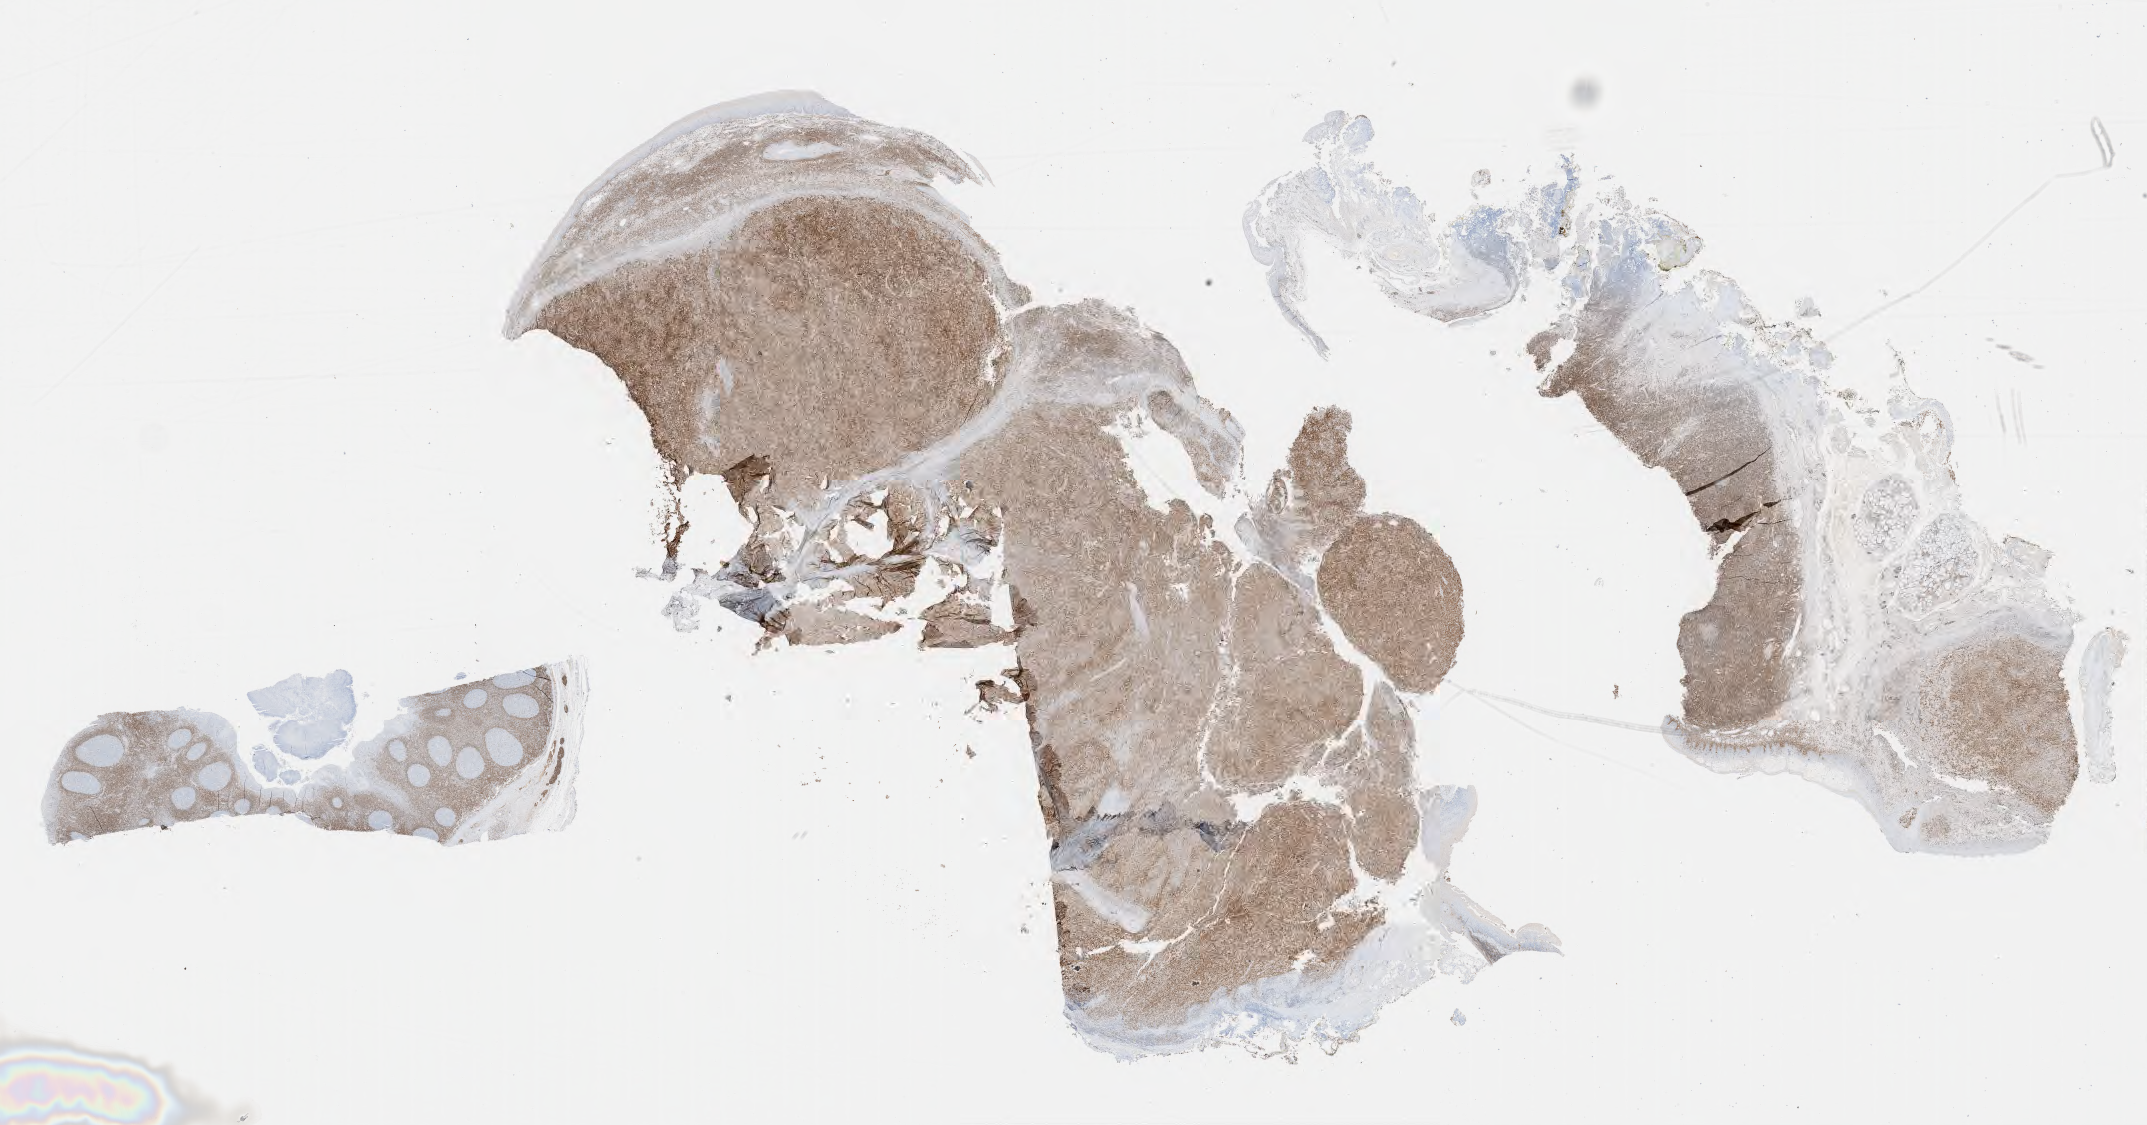
IHC for BCL2, whole-slide image, shown as a low-resolution overview of the whole scanned area (about 34.7 x 18.2 mm); tumor tissue; site: lymph node. Patient male; 56 years old.
Diagnosis: Diffuse large B-cell lymphoma, NOS.